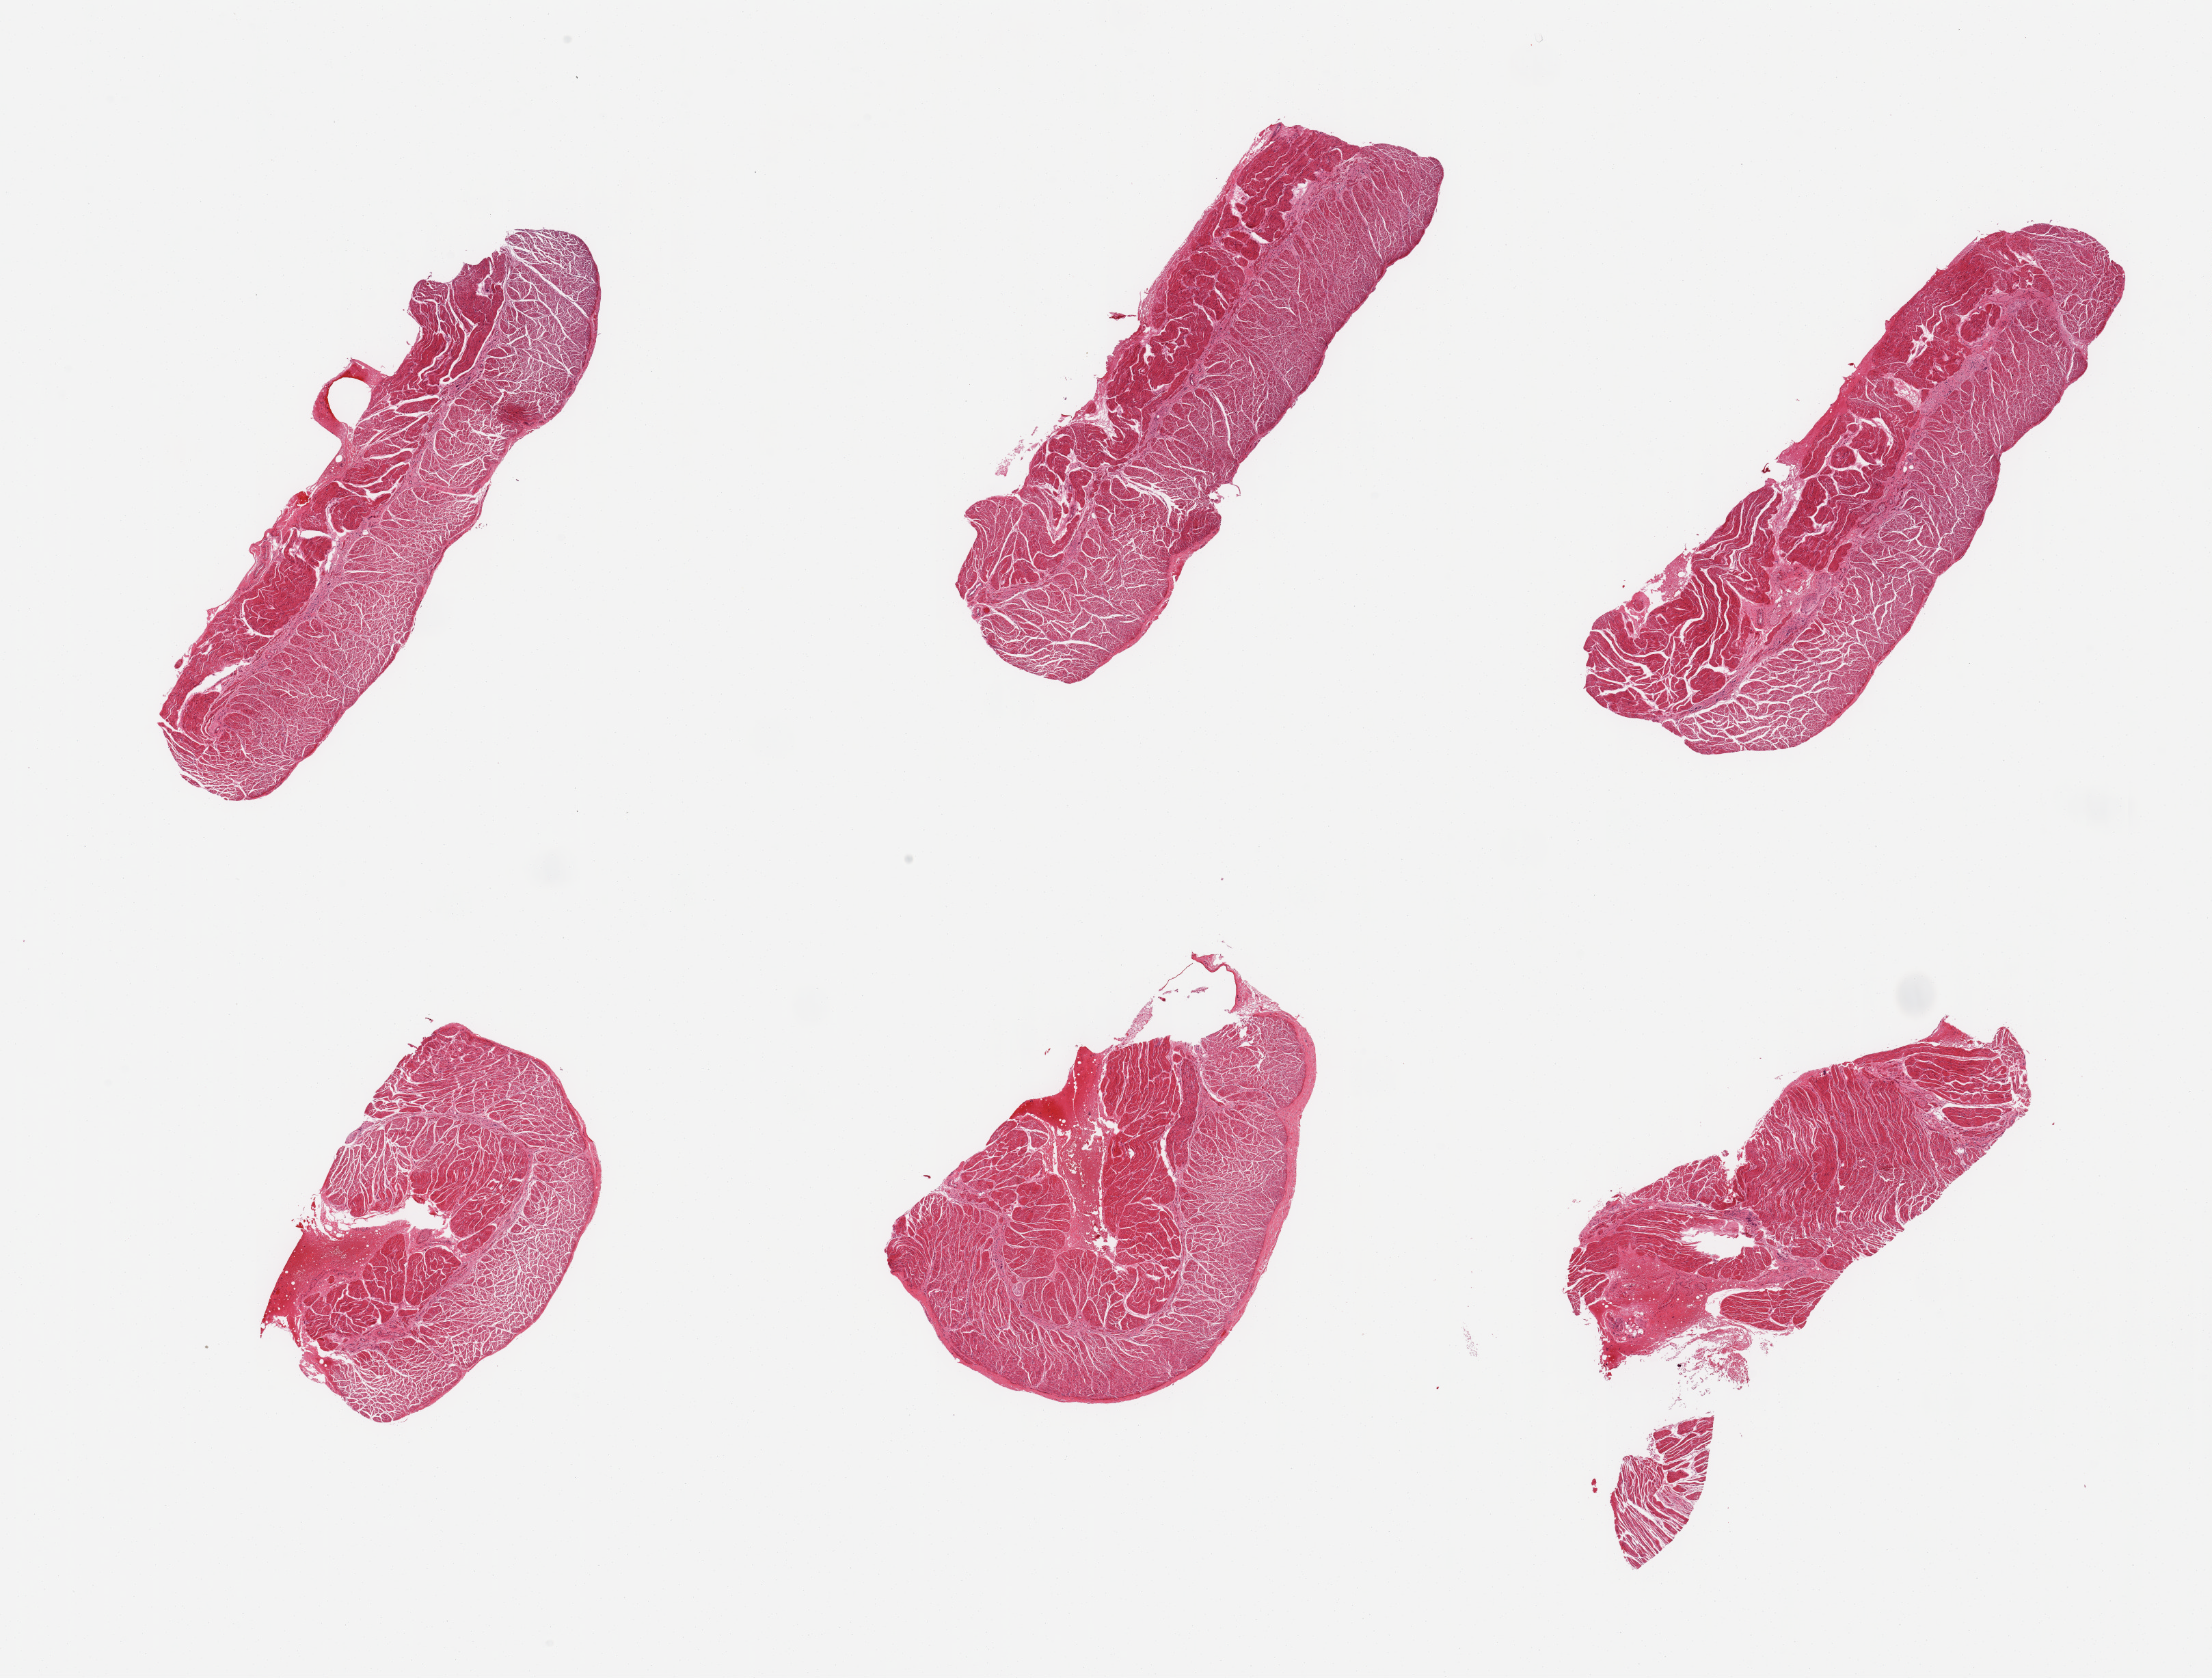
Digitized haematoxylin and eosin-stained section — a low-resolution overview of the entire scanned area, about 25.6 x 19.4 mm (from a 20x scan); PAXgene-fixed paraffin-embedded (PFPE) section; sampled site (target tissue): esophageal muscle; tissue donor sample. Donor sex: male.
Review note (as recorded): 6 pieces, confirmed target muscularis.